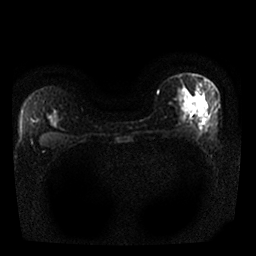
Breast MRI, one axial slice. Position 19 of 25 along the scan axis. Diffusion-weighted series; image 2 of 4 stored at this slice position (different b-values; order by instance number). 1.5 T. 4 mm slice thickness. 256 × 256 image matrix, field of view 320 × 320 mm. Female patient.
Structures marked on this image (expert manual segmentation):
- tumour on diffusion-weighted imaging: bounding box [x1, y1, x2, y2] px = [184, 99, 195, 110]